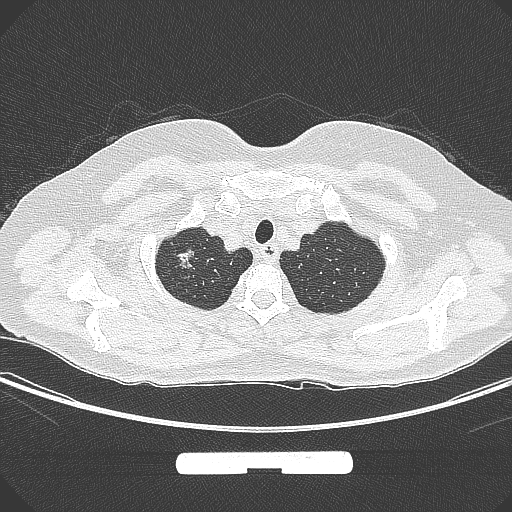
Chest CT, one axial slice; slice 262 of 295 in the series (ordered by position); 120 kVp; lung window (W 1500 / L -600 HU); 1 mm slice thickness; 512 × 512 image matrix. Female patient, age 58 years. From the clinical record (not read from this slice): clinical TNM (as recorded): T1b N0 M0; histopathological grade: G2-3.
Annotated regions visible in this slice (bounding box drawn by a radiologist):
- lung tumour (recorded histology: adenocarcinoma): box from (x=173, y=239) to (x=197, y=273) px